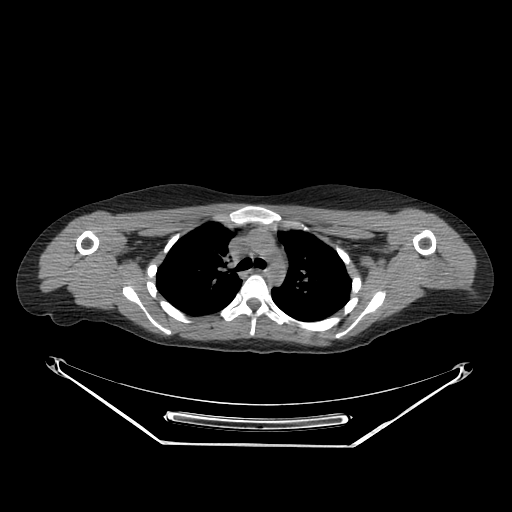
CT of an extremity soft-tissue mass (from a PET/CT study), one axial slice; slice 203 of 267 in the series (ordered by position); reconstruction kernel SOFT; 140 kVp; soft-tissue window (W 400 / L 40 HU); 3.75 mm slice thickness; 512 × 512 image matrix. Female patient. Case-level facts recorded for this patient, not image findings: histological type: malignant fibrous histiocytoma; grade: low; site of the primary tumour: left arm.
Annotated regions visible in this slice (expert contour drawn on MRI and transferred to this co-registered scan by the dataset authors):
- gross tumour volume (mass): bounding box <425,251,457,282> (left, top, right, bottom; pixels)